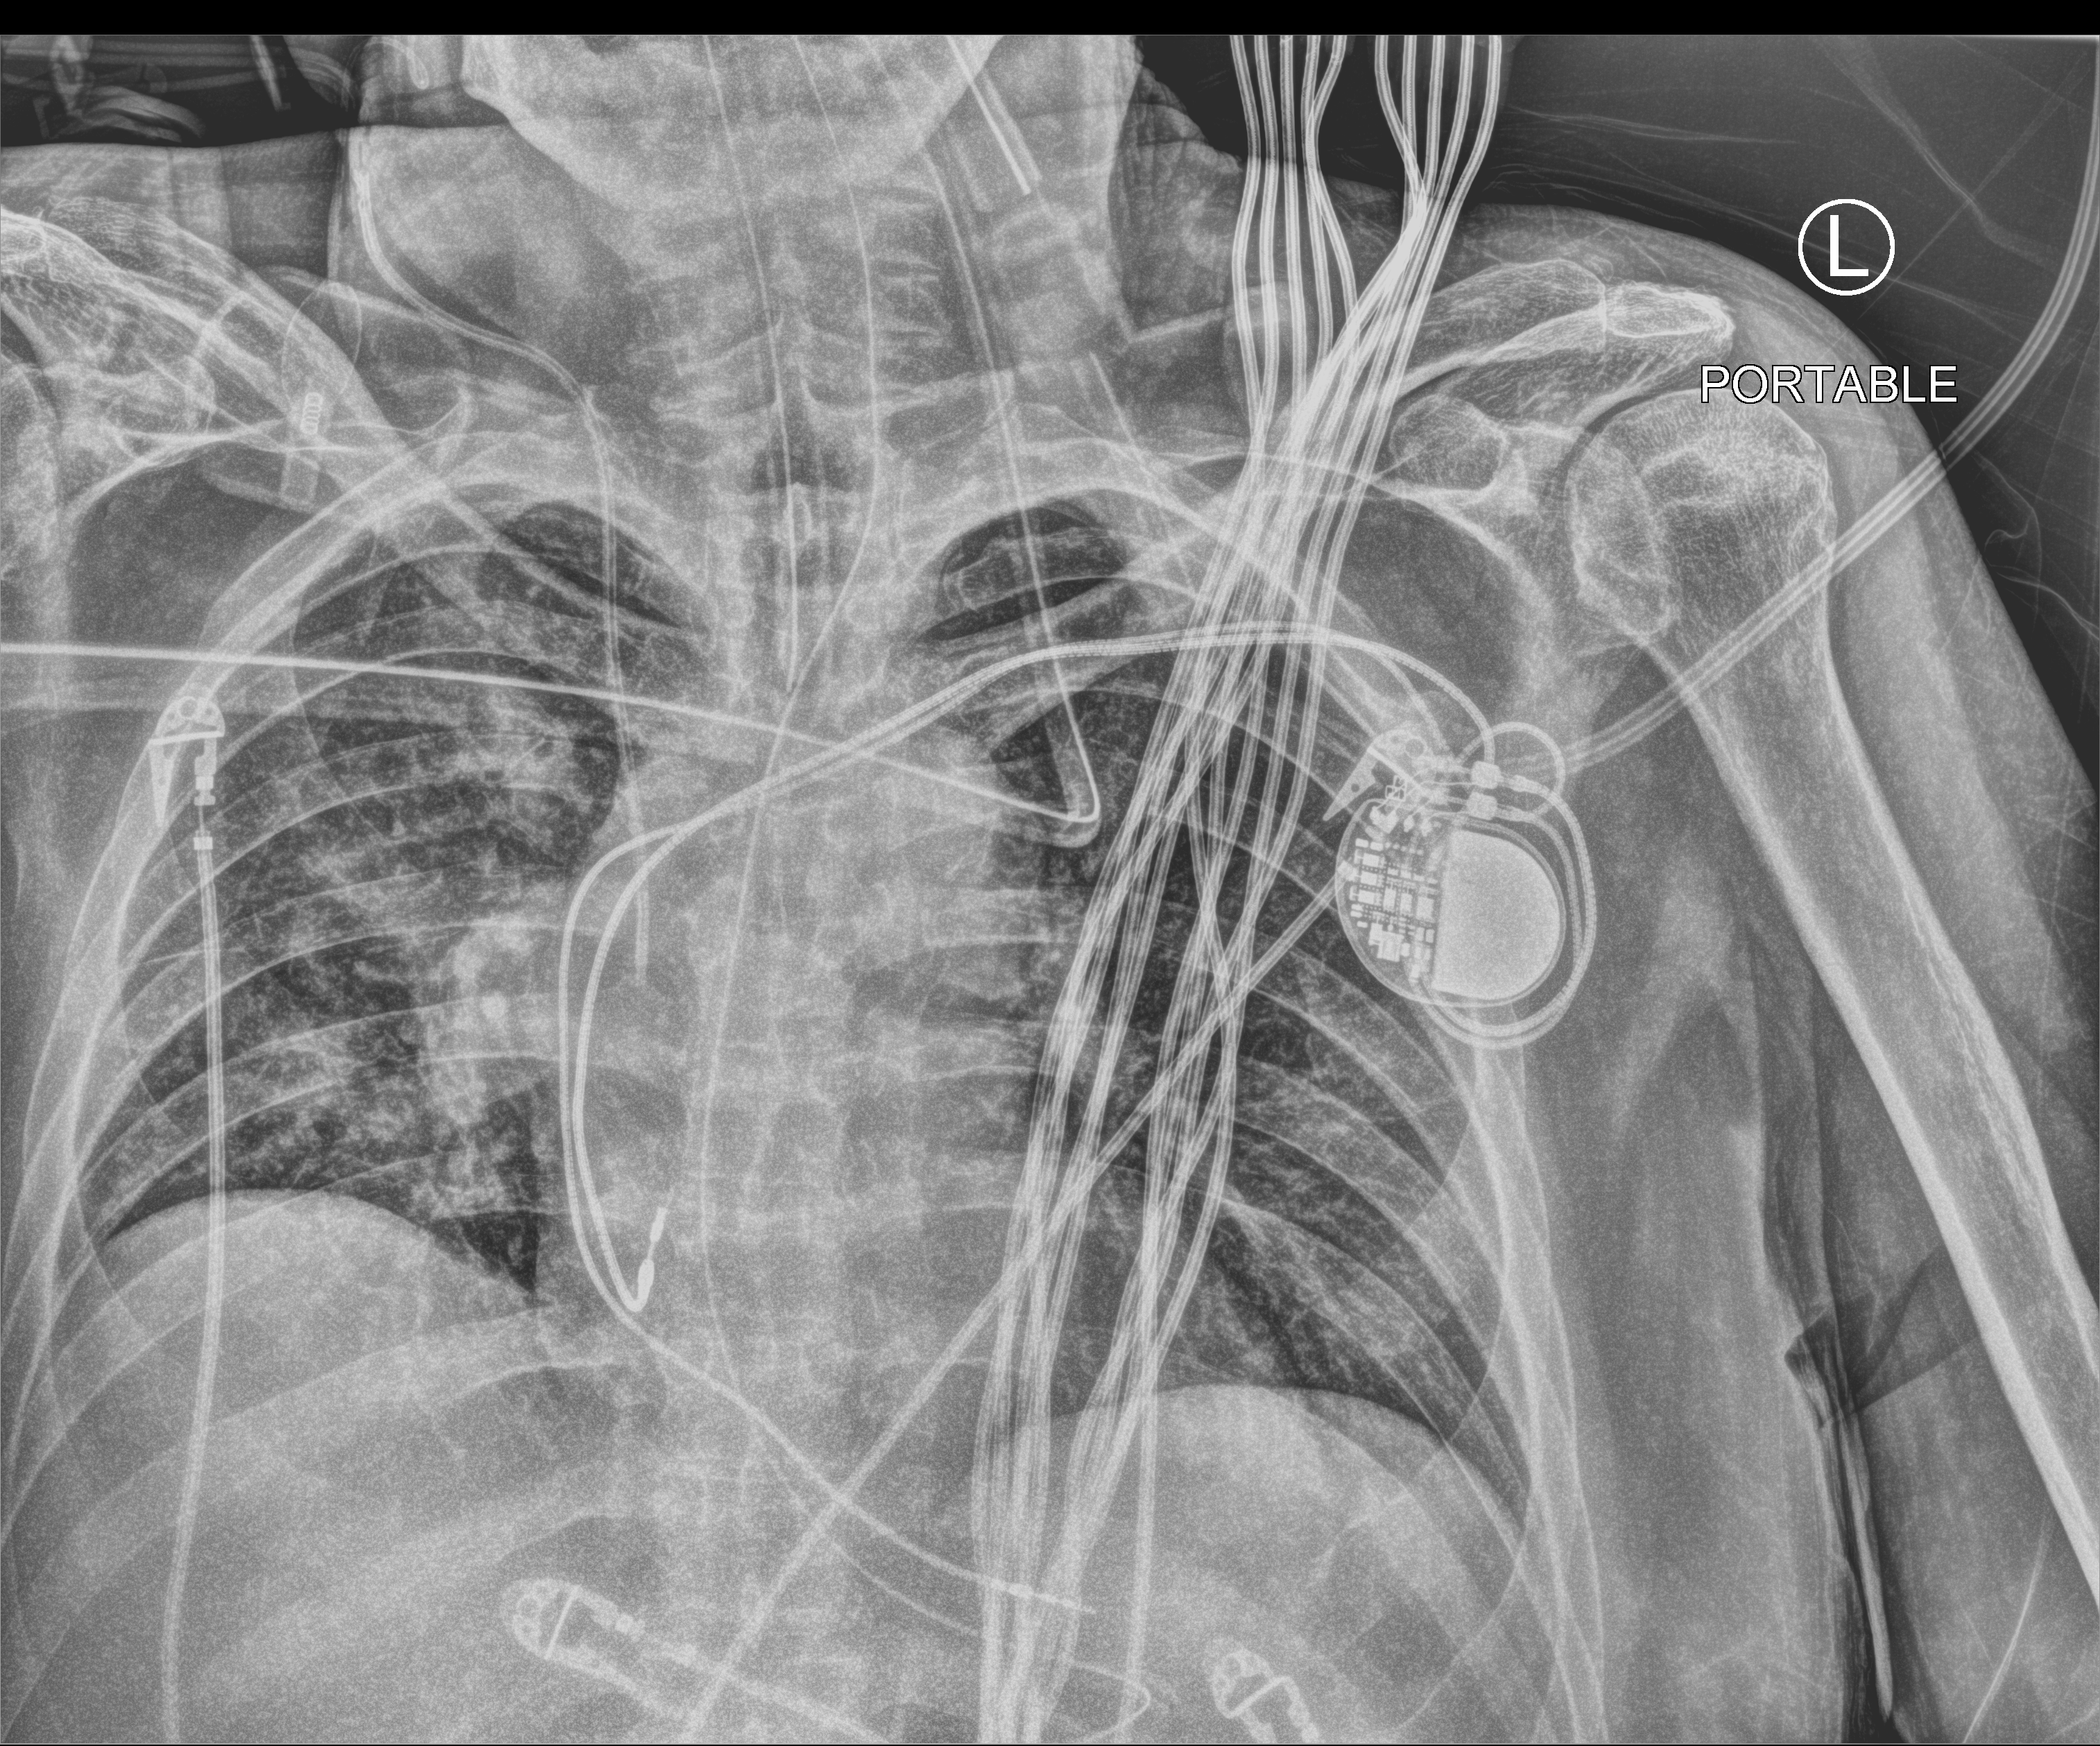
Bedside chest radiograph (computed radiography). Male patient hospitalised with COVID-19, age 60–74 years.
Hospital-stay facts (about this admission, not read from this image; timing relative to this image not recorded): mechanically ventilated during this hospital stay: no.